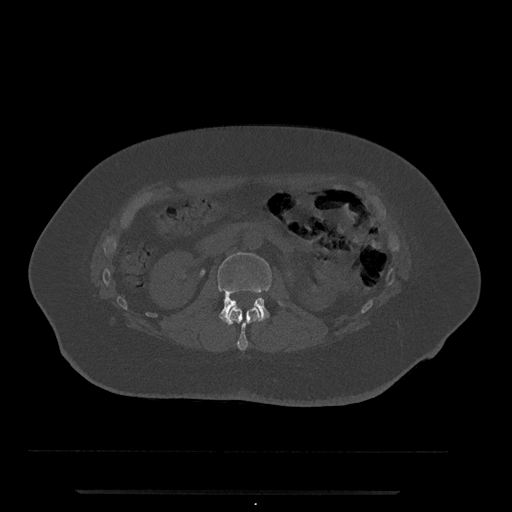
CT including the spine, one axial slice. Slice 62 of 797 in the series (ordered by position). Reconstruction kernel Br40s/3. 120 kVp. Bone window (W 1800 / L 400 HU). 512 × 512 image matrix, field of view 440 × 440 mm. Female patient, age 51 years. From the clinical record (not read from this slice): primary cancer: neuro.
Outlined on this slice (semi-automatically segmented with operator editing):
- L1 vertebra: bounding box <224,307,261,350> (left, top, right, bottom; pixels)
- L2 vertebra: <217,252,283,322>